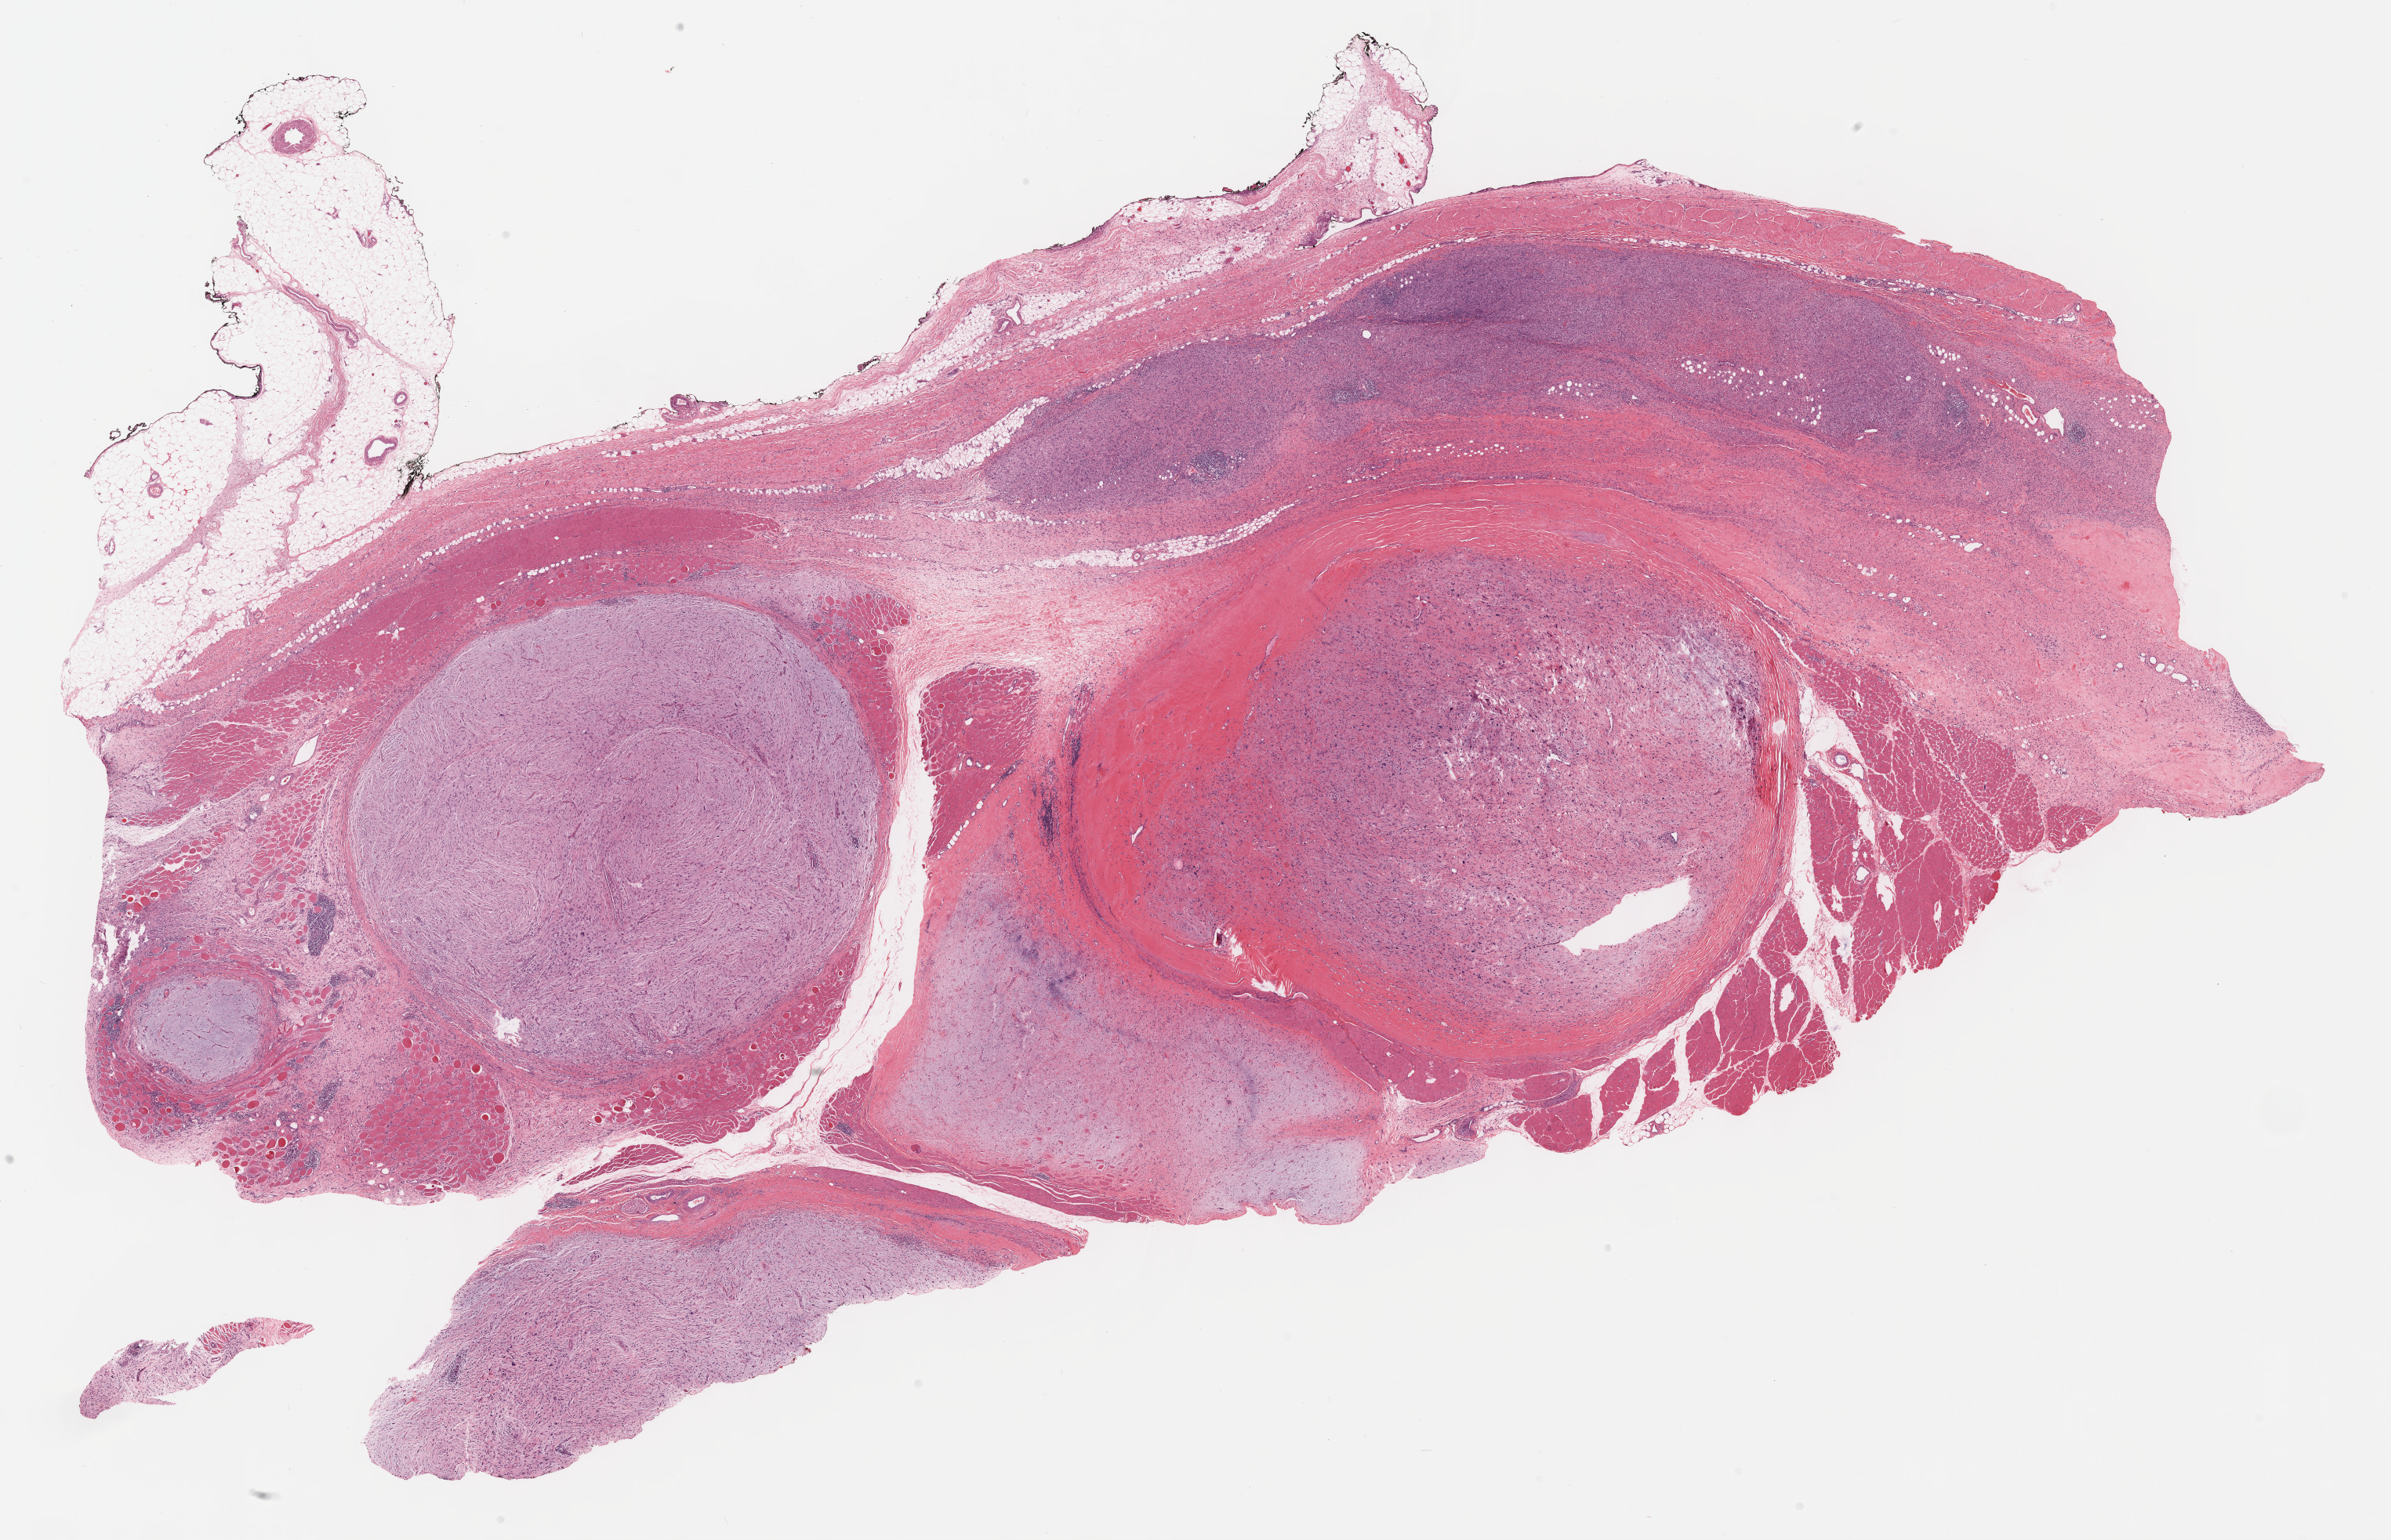
H&E-stained whole-slide image — a low-resolution overview of the entire scanned area, about 24.7 x 15.9 mm. Formalin-fixed paraffin-embedded (FFPE) diagnostic section. Sample: primary tumour, connective, subcutaneous and other soft tissues. Patient: female, age at initial diagnosis 78 years.
Diagnosis: Fibromyxosarcoma (connective, subcutaneous and other soft tissues of lower limb and hip).